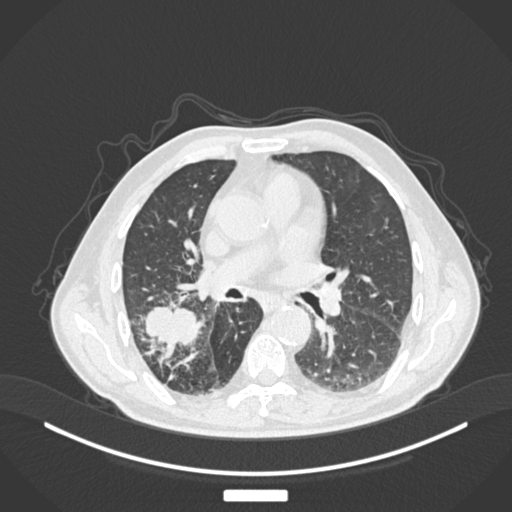
Chest CT, one axial slice. Position 90 of 201 along the scan axis. Reconstruction kernel B30f. 120 kVp. Lung window (W 1500 / L -600 HU). 1 mm slice thickness. 512 × 512 image matrix, field of view 400 × 400 mm. Patient: male, 72 years. Case-level facts recorded for this patient, not image findings: clinical TNM (as recorded): T3 N2 M0.
Structures marked on this image (bounding box drawn by a radiologist):
- lung tumour (recorded histology: adenocarcinoma): bounding box <140,297,204,350> (left, top, right, bottom; pixels)